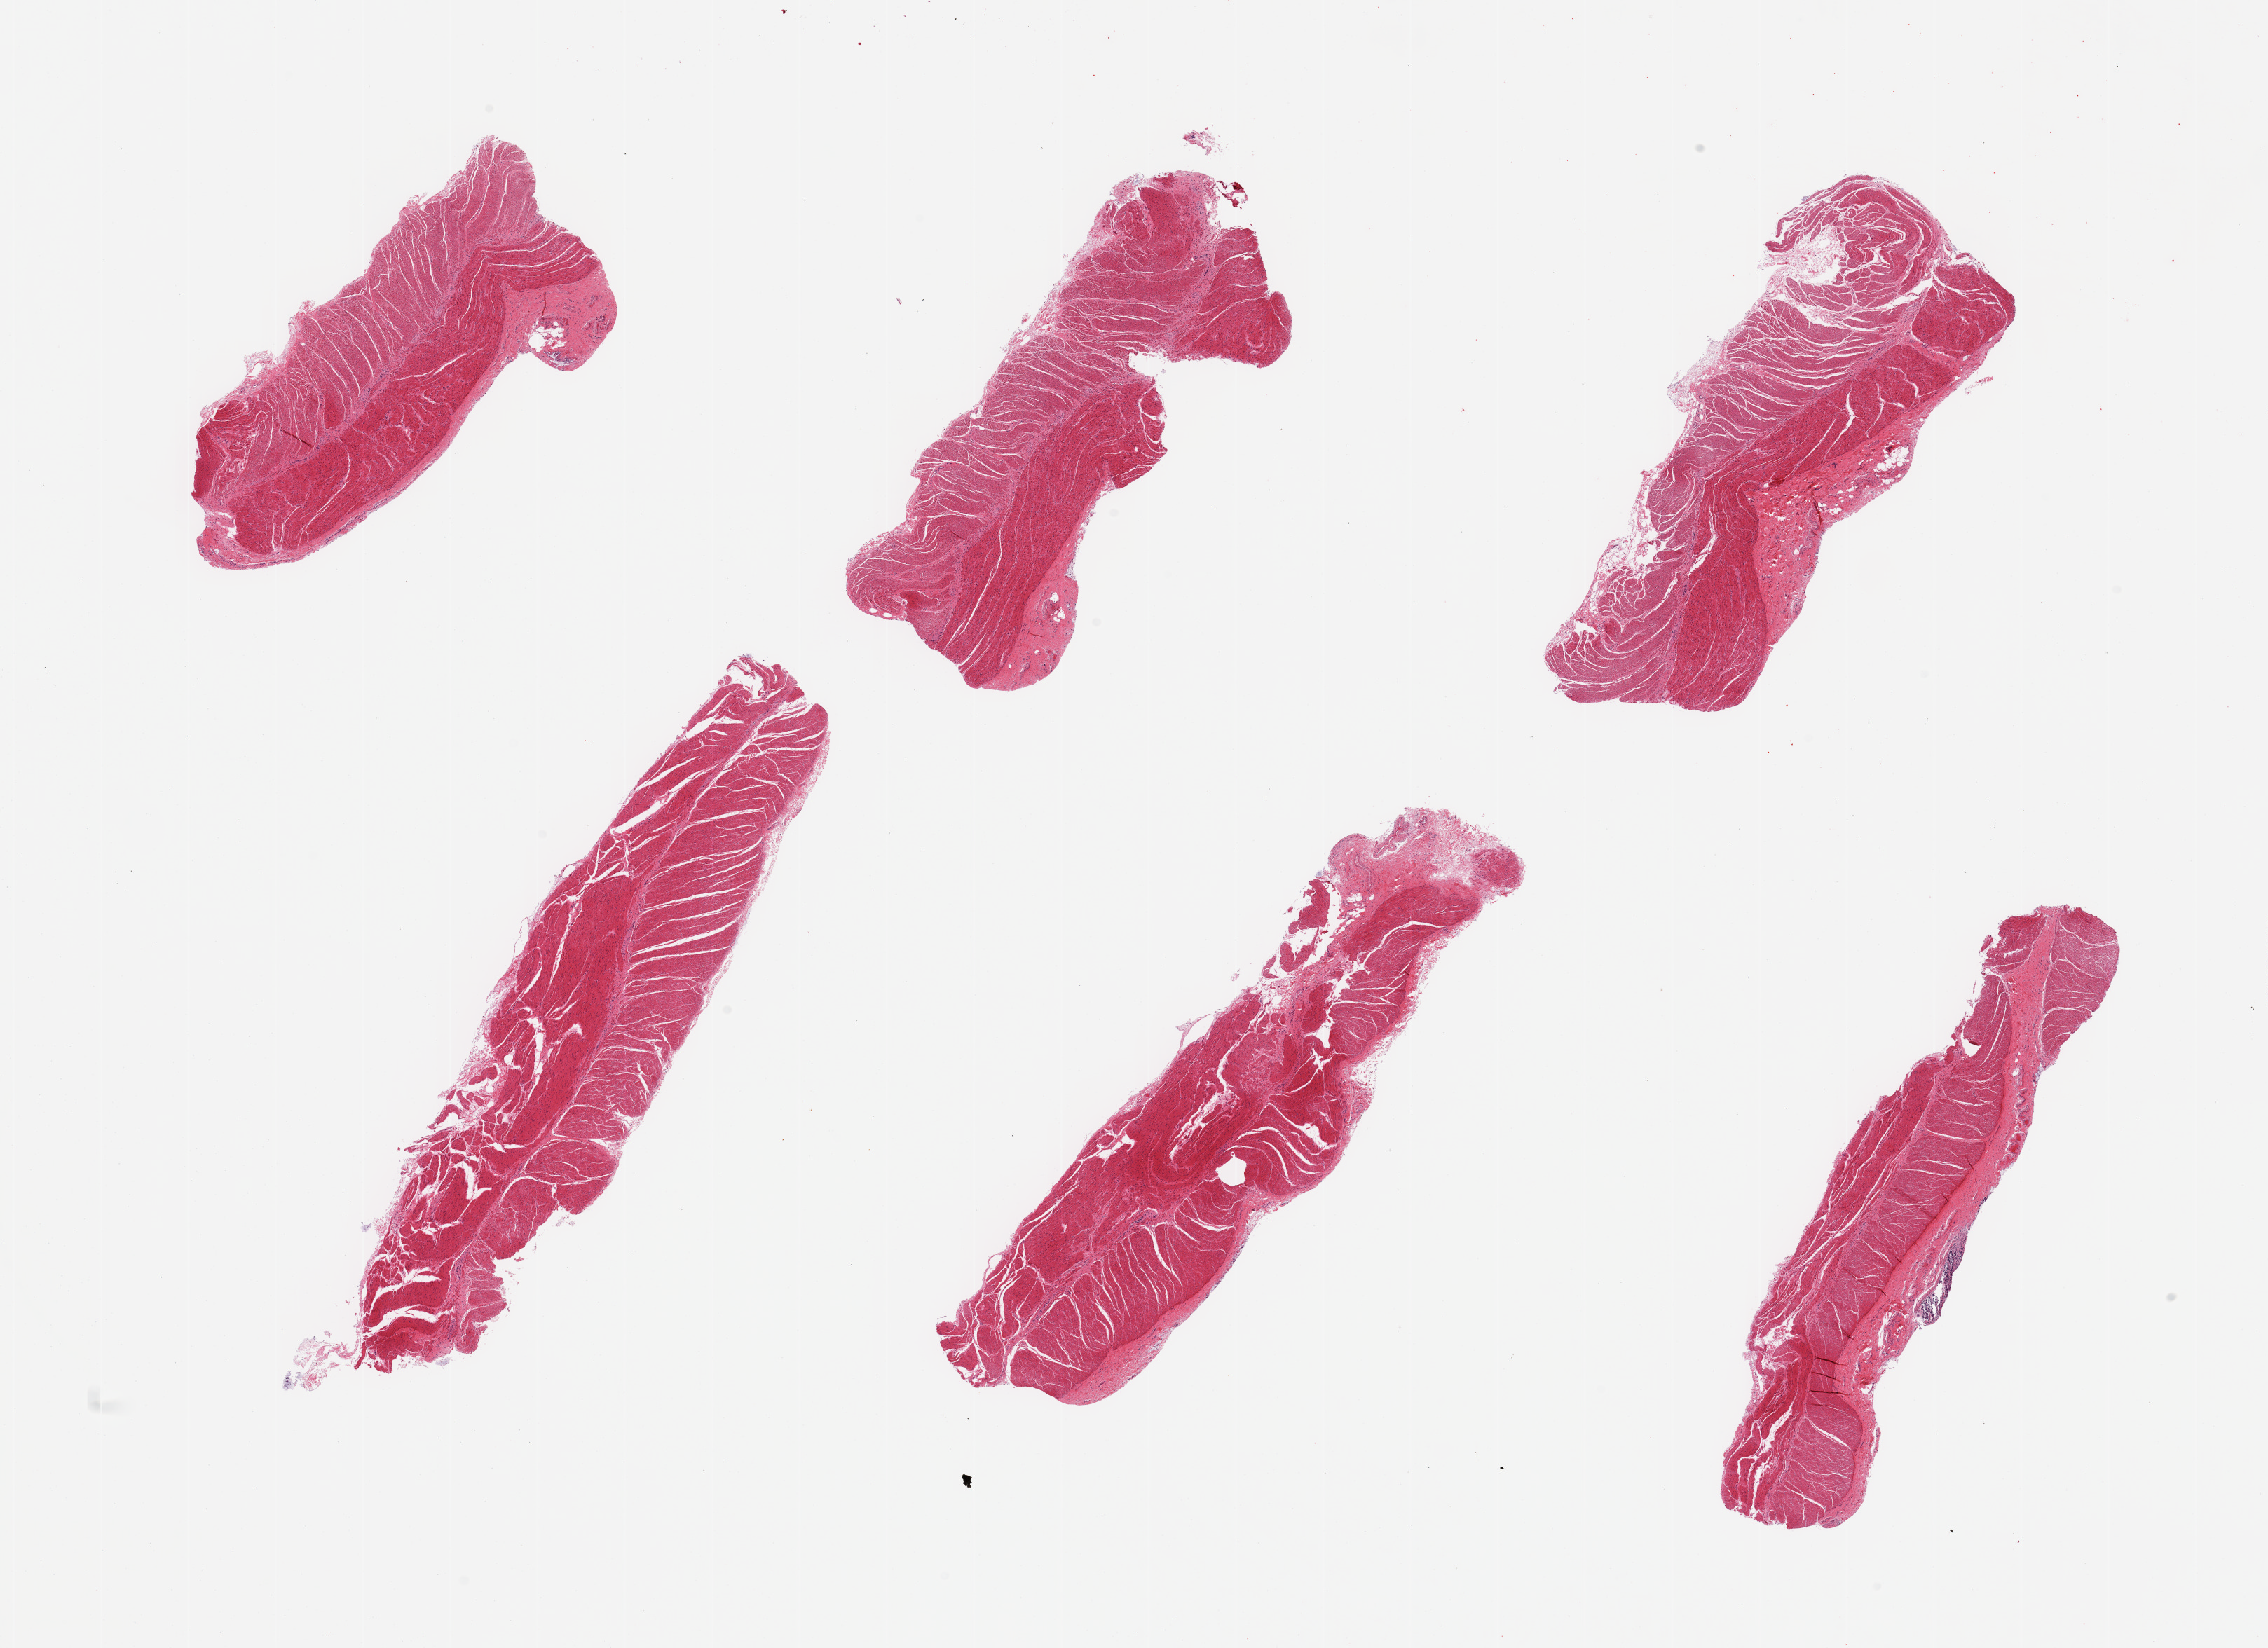
Whole-slide image, haematoxylin and eosin stain — whole scanned area (about 25.6 x 18.6 mm, acquisition: 20x scan) shown as a low-resolution overview. PAXgene-fixed paraffin-embedded (PFPE) section. Sampled site (target tissue): sigmoid colon. Donor tissue sample. Donor: male.
- reviewer comment on this tissue sample: 6 pieces, confirmed target muscularis